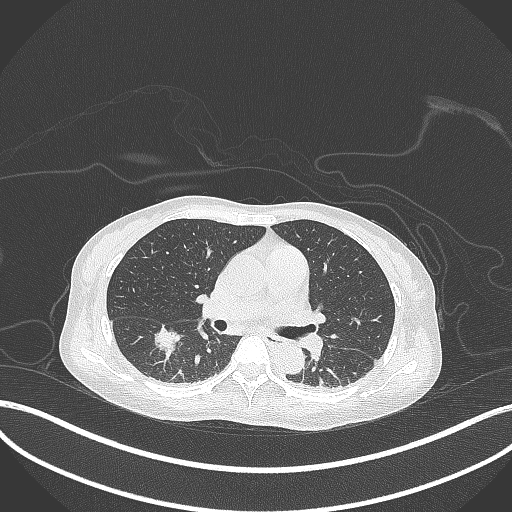
Chest CT, one axial slice. Slice 173 of 261 in the series (ordered by position). 120 kVp. Lung window (W 1500 / L -600 HU). 1 mm slice thickness. 512 × 512 image matrix, field of view 400 × 400 mm. Female patient, age 44 years. From the clinical record (not read from this slice): clinical TNM (as recorded): T1c N0 M0.
Outlined on this slice (rectangle marked by the reading radiologist):
- lung tumour (recorded histology: adenocarcinoma): bounding box (x1, y1, x2, y2) in pixels: (155, 325, 185, 360)